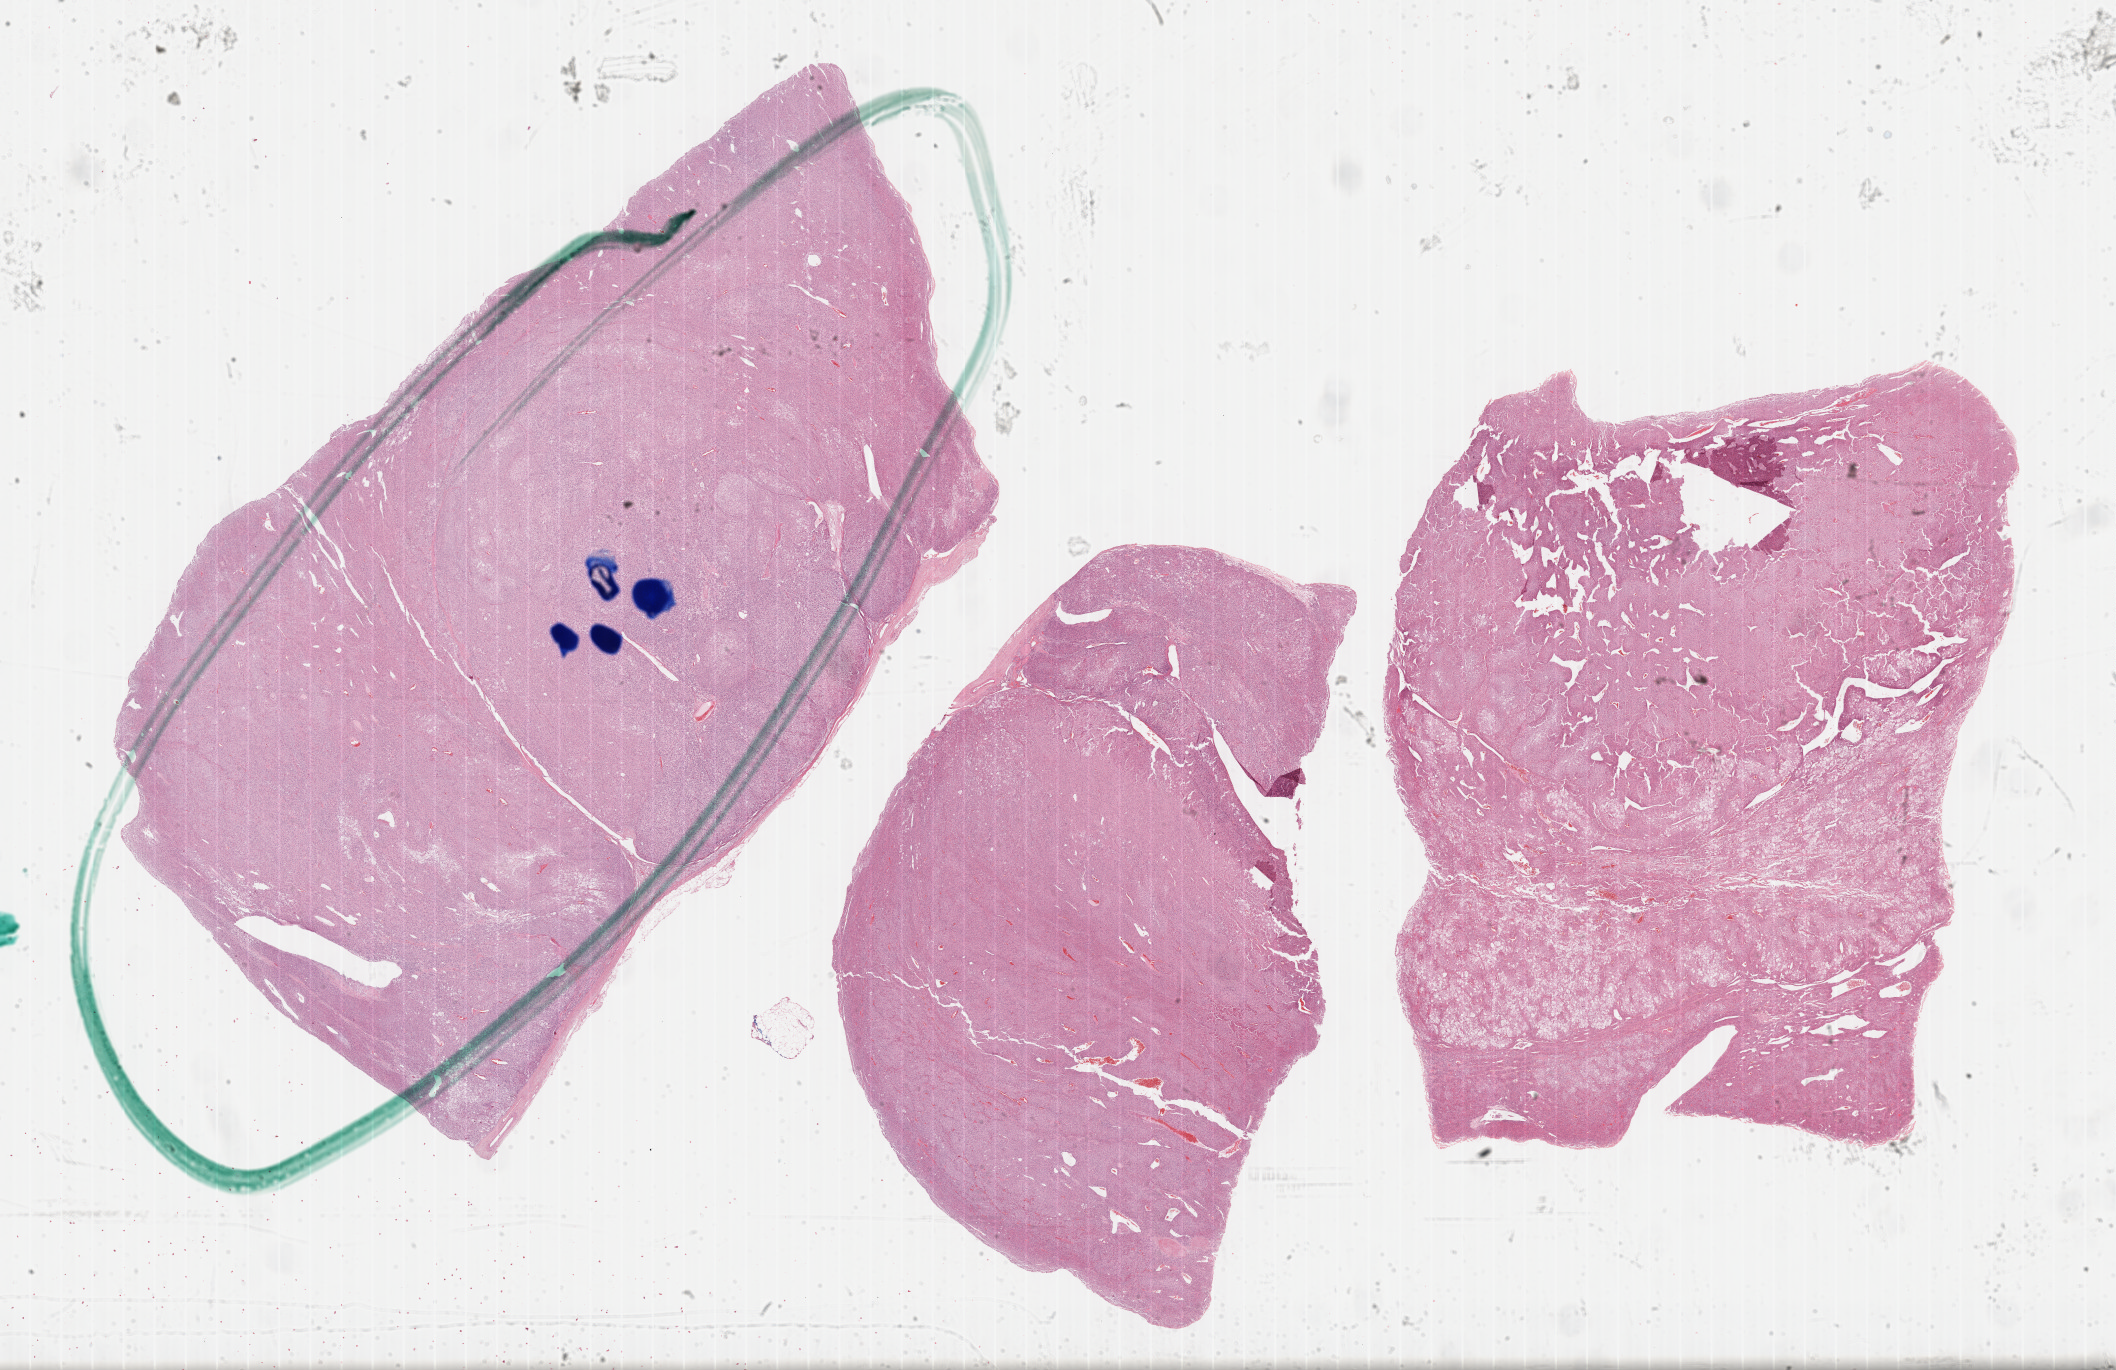
Digitized Hematoxylin and eosin (H&E) stained tissue section (whole slide) — whole scanned area (about 34.2 x 22.2 mm) shown as a low-resolution overview, formalin-fixed paraffin-embedded (FFPE) diagnostic section, adrenal cortex, primary tumour sample. Patient: male, age at initial diagnosis 47 years.
Pathologic diagnosis: Adrenal cortical carcinoma (cortex of adrenal gland).